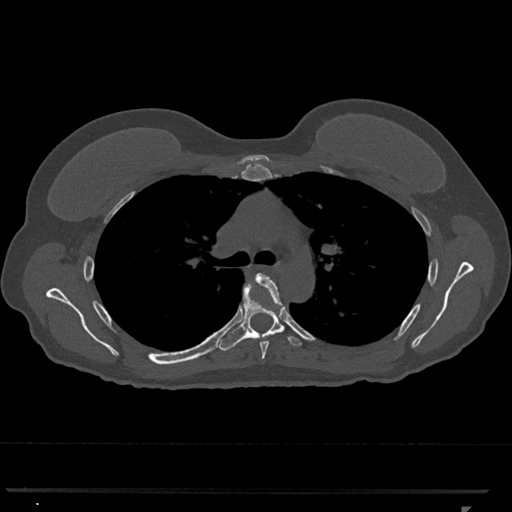
CT including the spine, one axial slice. Slice 781 of 793 in the series (ordered by position). 120 kVp. Bone window (W 1800 / L 400 HU). 0.5 mm slice thickness. 512 × 512 image matrix, field of view 380 × 380 mm. Patient: female, 62 years. Case-level facts recorded for this patient, not image findings: primary cancer: renal.
Annotated regions visible in this slice (semi-automatic segmentation, software-assisted and operator-edited):
- T5 vertebra: bounding box (x1, y1, x2, y2) in pixels: (256, 273, 282, 359)
- T6 vertebra: (219, 280, 302, 351)